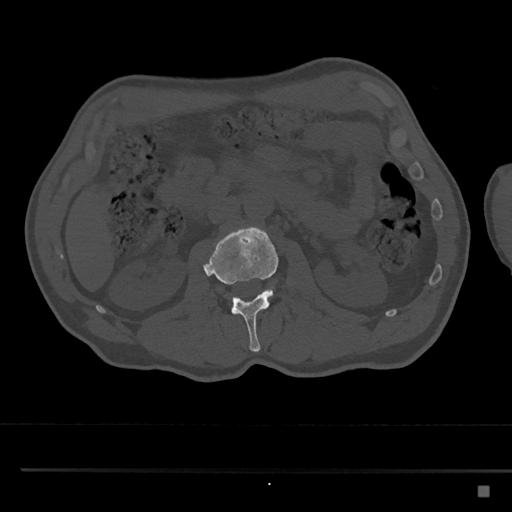
CT including the spine, one axial slice. Slice 748 of 797 in the series (ordered by position). 120 kVp. Bone window (W 1800 / L 400 HU). 0.5 mm slice thickness. 512 × 512 image matrix, field of view 391 × 391 mm. Patient: male, 59 years. From the clinical record (not read from this slice): primary cancer: prostate.
Structures marked on this image (semi-automatic segmentation, software-assisted and operator-edited):
- L2 vertebra: box from (x=203, y=226) to (x=279, y=352) px